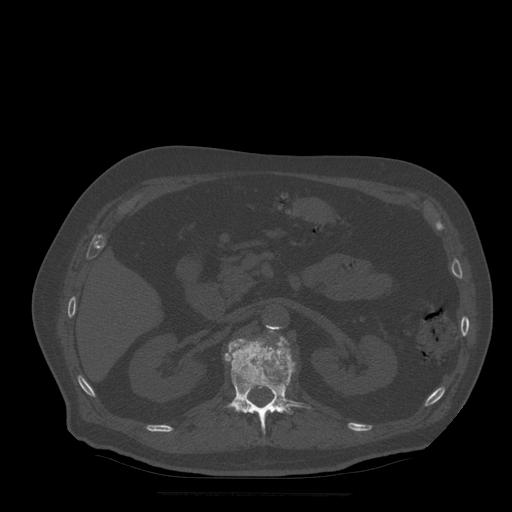
CT including the spine, one axial slice; position 195 of 522 along the scan axis; bone window (W 1800 / L 400 HU); 512 × 512 image matrix, field of view 420 × 420 mm. Patient age 72 years. Case-level facts recorded for this patient, not image findings: primary cancer: prostate.
Annotated regions visible in this slice (semi-automatic segmentation, software-assisted and operator-edited):
- L1 vertebra: box from (x=225, y=337) to (x=311, y=434) px
- L2 vertebra: (x=269, y=331)–(x=275, y=334)